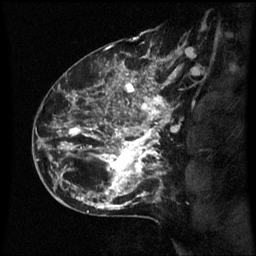
Breast MRI (dynamic contrast-enhanced), one sagittal slice; position 43 of 60 along the scan axis; dynamic contrast-enhanced series, image 2 of 3 at this slice position (ordered by acquisition); 1.5 T; TE 4.2 ms, TR 8.9 ms; 256 × 256 image matrix, field of view 200 × 200 mm. Female patient, age 42 years. Case-level facts recorded for this patient, not image findings: setting: breast cancer imaged before/during neoadjuvant chemotherapy; receptor status: HER2-positive.
Structures marked on this image (semi-automatically segmented with operator editing):
- analysis volume of interest (the breast-tissue region the enhancement analysis was run in; not a lesion): box from (x=66, y=82) to (x=173, y=193) px
- tumour enhancement mask (voxels above the 70 % enhancement threshold inside the analysis volume of interest): (x=66, y=82)–(x=171, y=193)